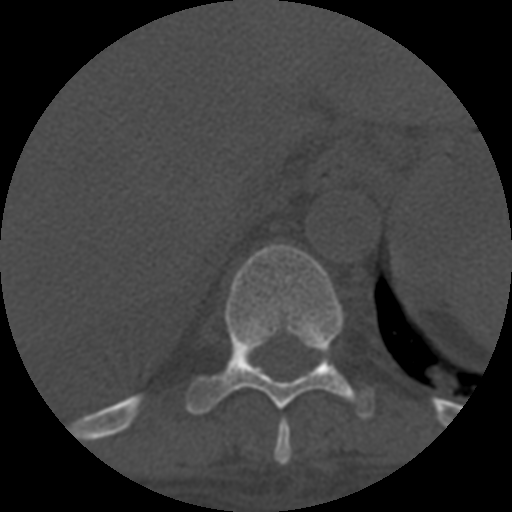
CT including the spine, one axial slice; slice 358 of 708 in the series (ordered by position); reconstruction kernel STANDARD; one of 3 acquisitions stored at this slice position; bone window (W 1800 / L 400 HU); 1.25 mm slice thickness; 512 × 512 image matrix, field of view 160 × 160 mm. Patient age 55 years. Case-level facts recorded for this patient, not image findings: primary cancer: colon; vertebrae with lytic lesions (as recorded): T12, L1, L5.
Structures marked on this image (semi-automatically segmented with operator editing):
- T10 vertebra: bounding box (x1, y1, x2, y2) in pixels: (186, 244, 375, 419)
- T9 vertebra: (274, 420, 292, 465)